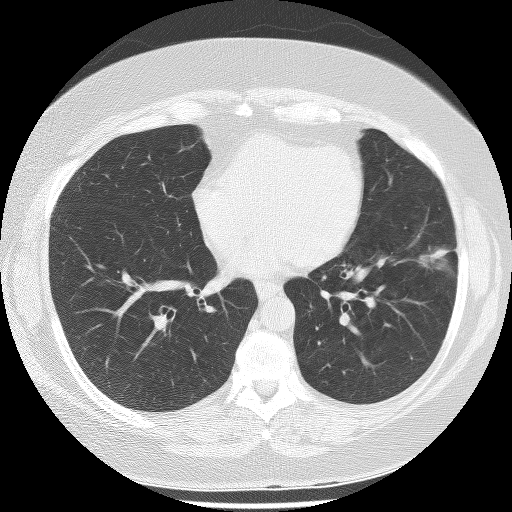
Chest CT (low-dose screening protocol), one axial image. Baseline screening round. Lung window (W 1500 / L -600 HU). 2.5 mm slice thickness. Female participant, aged 56 years at enrolment.
Expert-annotated lung lesion, bounding box (x1, y1, x2, y2) in pixels: (401, 231, 464, 281). Screening reader's record for this exam (one nodule recorded; not confirmed to be the boxed lesion): non-calcified nodule or mass ≥4 mm, left lower lobe, 22 × 17 mm, spiculated (stellate) margins, soft tissue attenuation. Official screen result: positive, change unspecified: nodule(s) >= 4 mm or enlarging nodule(s), mass(es), or other non-specific abnormalities suspicious for lung cancer.